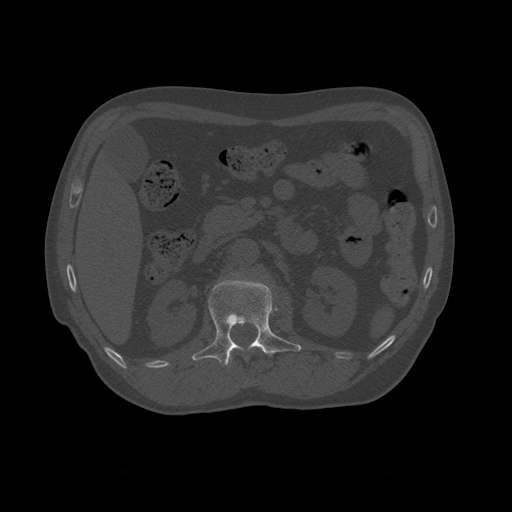
CT including the spine, one axial slice. Position 355 of 450 along the scan axis. Reconstruction kernel STANDARD. Bone window (W 1800 / L 400 HU). 1.25 mm slice thickness. 512 × 512 image matrix, field of view 405 × 405 mm. Patient age 75 years. From the clinical record (not read from this slice): primary cancer: prostate.
Annotated regions visible in this slice (semi-automatic segmentation, software-assisted and operator-edited):
- L1 vertebra: bounding box [x1, y1, x2, y2] px = [192, 273, 302, 366]
- T10 vertebra: [224, 349, 262, 365]
- T11 vertebra: [226, 357, 232, 366]